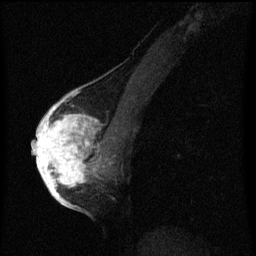
Breast MRI (dynamic contrast-enhanced), one sagittal slice; position 30 of 60 along the scan axis; dynamic contrast-enhanced series, image 2 of 3 at this slice position (ordered by acquisition); 1.5 T; TE 4.2 ms, TR 8 ms; 256 × 256 image matrix. Patient: female, 56 years.
Structures marked on this image (semi-automatic segmentation, software-assisted and operator-edited):
- analysis volume of interest (the breast-tissue region the enhancement analysis was run in; not a lesion): bounding box [x1, y1, x2, y2] px = [42, 110, 107, 193]
- tumour enhancement mask (voxels above the 70 % enhancement threshold inside the analysis volume of interest): [42, 110, 97, 193]